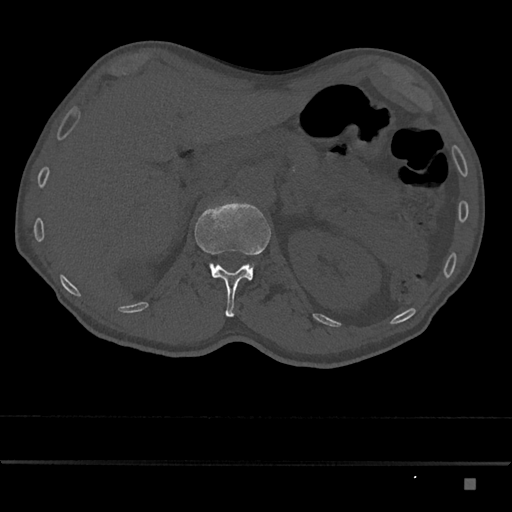
CT including the spine, one axial slice; reconstruction kernel Br40s/3; 120 kVp; bone window (W 1800 / L 400 HU); 0.5 mm slice thickness; 512 × 512 image matrix, field of view 390 × 390 mm. Male patient, age 72 years. From the clinical record (not read from this slice): primary cancer: prostate.
Structures marked on this image (semi-automatically segmented with operator editing):
- L1 vertebra: bounding box [x1, y1, x2, y2] px = [194, 201, 271, 317]